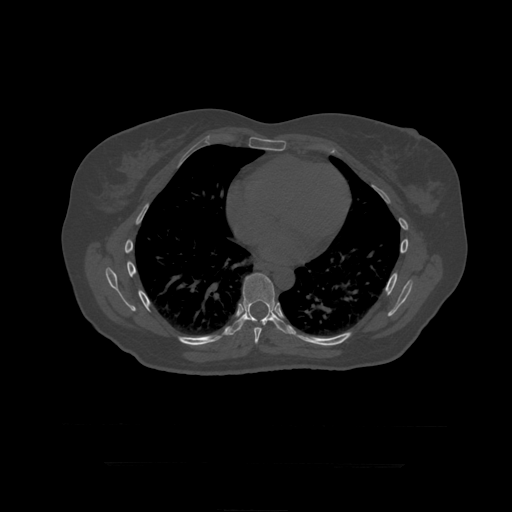
CT including the spine, one axial slice. Position 269 of 399 along the scan axis. Reconstruction kernel STANDARD. 120 kVp. Bone window (W 1800 / L 400 HU). 512 × 512 image matrix, field of view 450 × 450 mm. Patient age 41 years. Case-level facts recorded for this patient, not image findings: primary cancer: breast.
Outlined on this slice (semi-automatically segmented with operator editing):
- T8 vertebra: bounding box (x1, y1, x2, y2) in pixels: (254, 327, 262, 344)
- T9 vertebra: (227, 273, 291, 335)